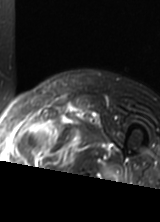
MRI of an extremity soft-tissue mass, one axial slice; slice 50 of 69 in the series (ordered by position); T2-weighted fat-saturated; MR volume resampled by the dataset authors to the PET/CT grid (not the native acquisition matrix); 3.27 mm slice thickness; 160 × 222 image matrix, field of view 156 × 217 mm. Female patient. From the clinical record (not read from this slice): histological type: pleomorphic leiomyosarcoma; grade: high; site of the primary tumour: left thigh.
Annotated regions visible in this slice (expert contour drawn on MRI and transferred to this co-registered scan by the dataset authors):
- gross tumour volume including surrounding oedema: bounding box <18,118,78,162> (left, top, right, bottom; pixels)